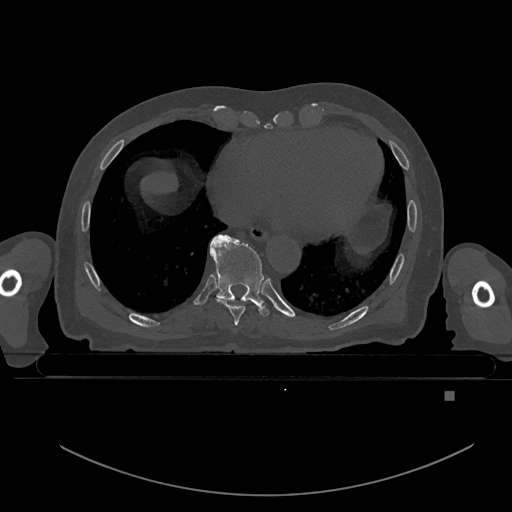
CT including the spine, one axial slice. Position 169 of 969 along the scan axis. Bone window (W 1800 / L 400 HU). 0.5 mm slice thickness. 512 × 512 image matrix, field of view 456 × 456 mm. Male patient, age 82 years. From the clinical record (not read from this slice): primary cancer: prostate; vertebrae with lytic lesions (as recorded): T11, T9, T8, T2.
Structures marked on this image (semi-automatic segmentation, software-assisted and operator-edited):
- T8 vertebra: bounding box [x1, y1, x2, y2] px = [215, 297, 251, 326]
- T9 vertebra: [210, 235, 270, 317]